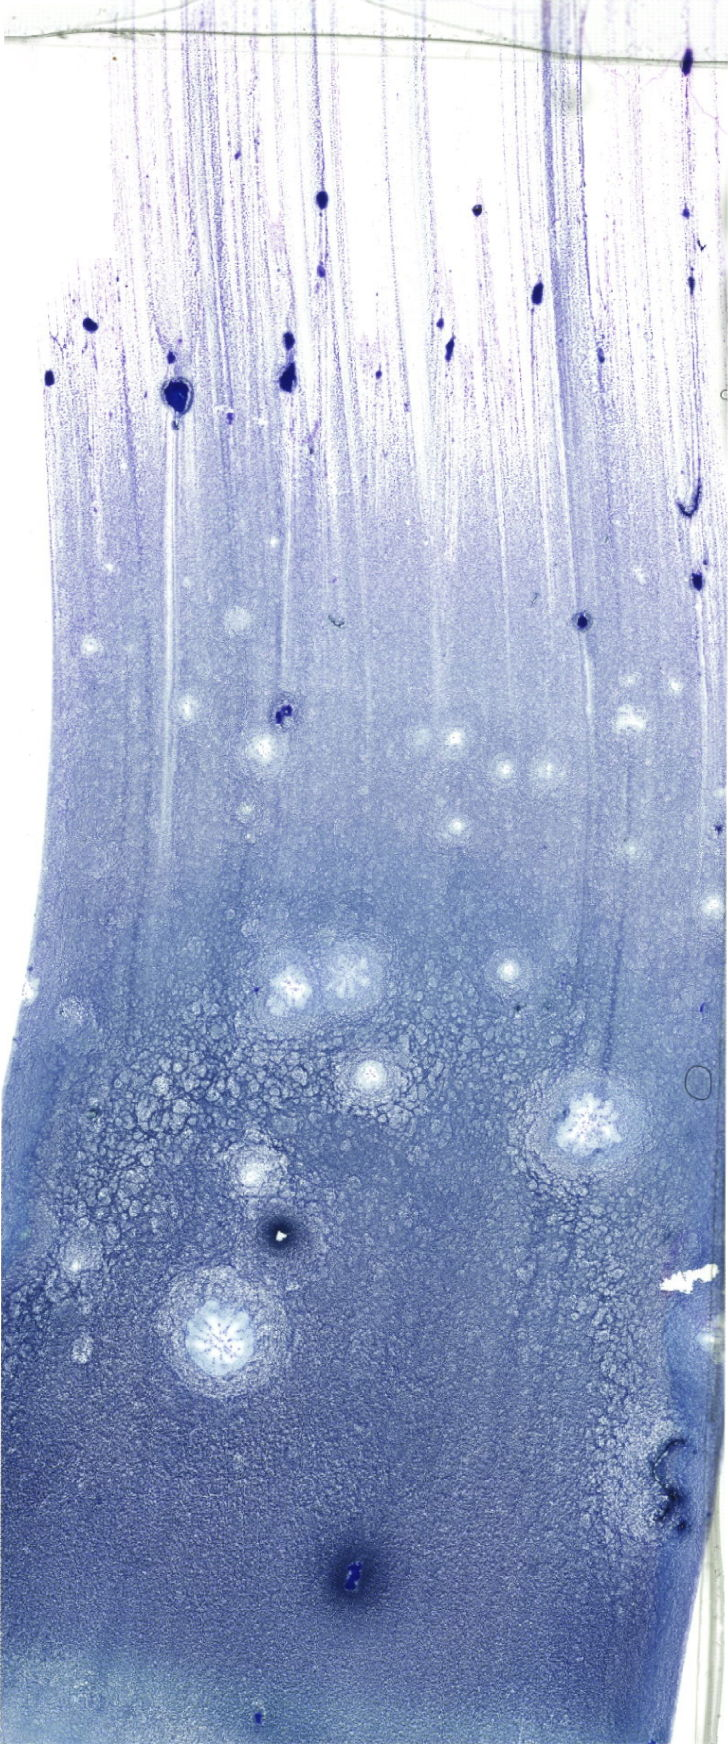
May-Grünwald–Giemsa-stained marrow aspirate smear (whole slide), shown as a low-resolution overview of the whole scanned area (about 20.6 x 49.4 mm). Female patient.
Diagnosis: B Acute Lymphoblastic Leukemia.